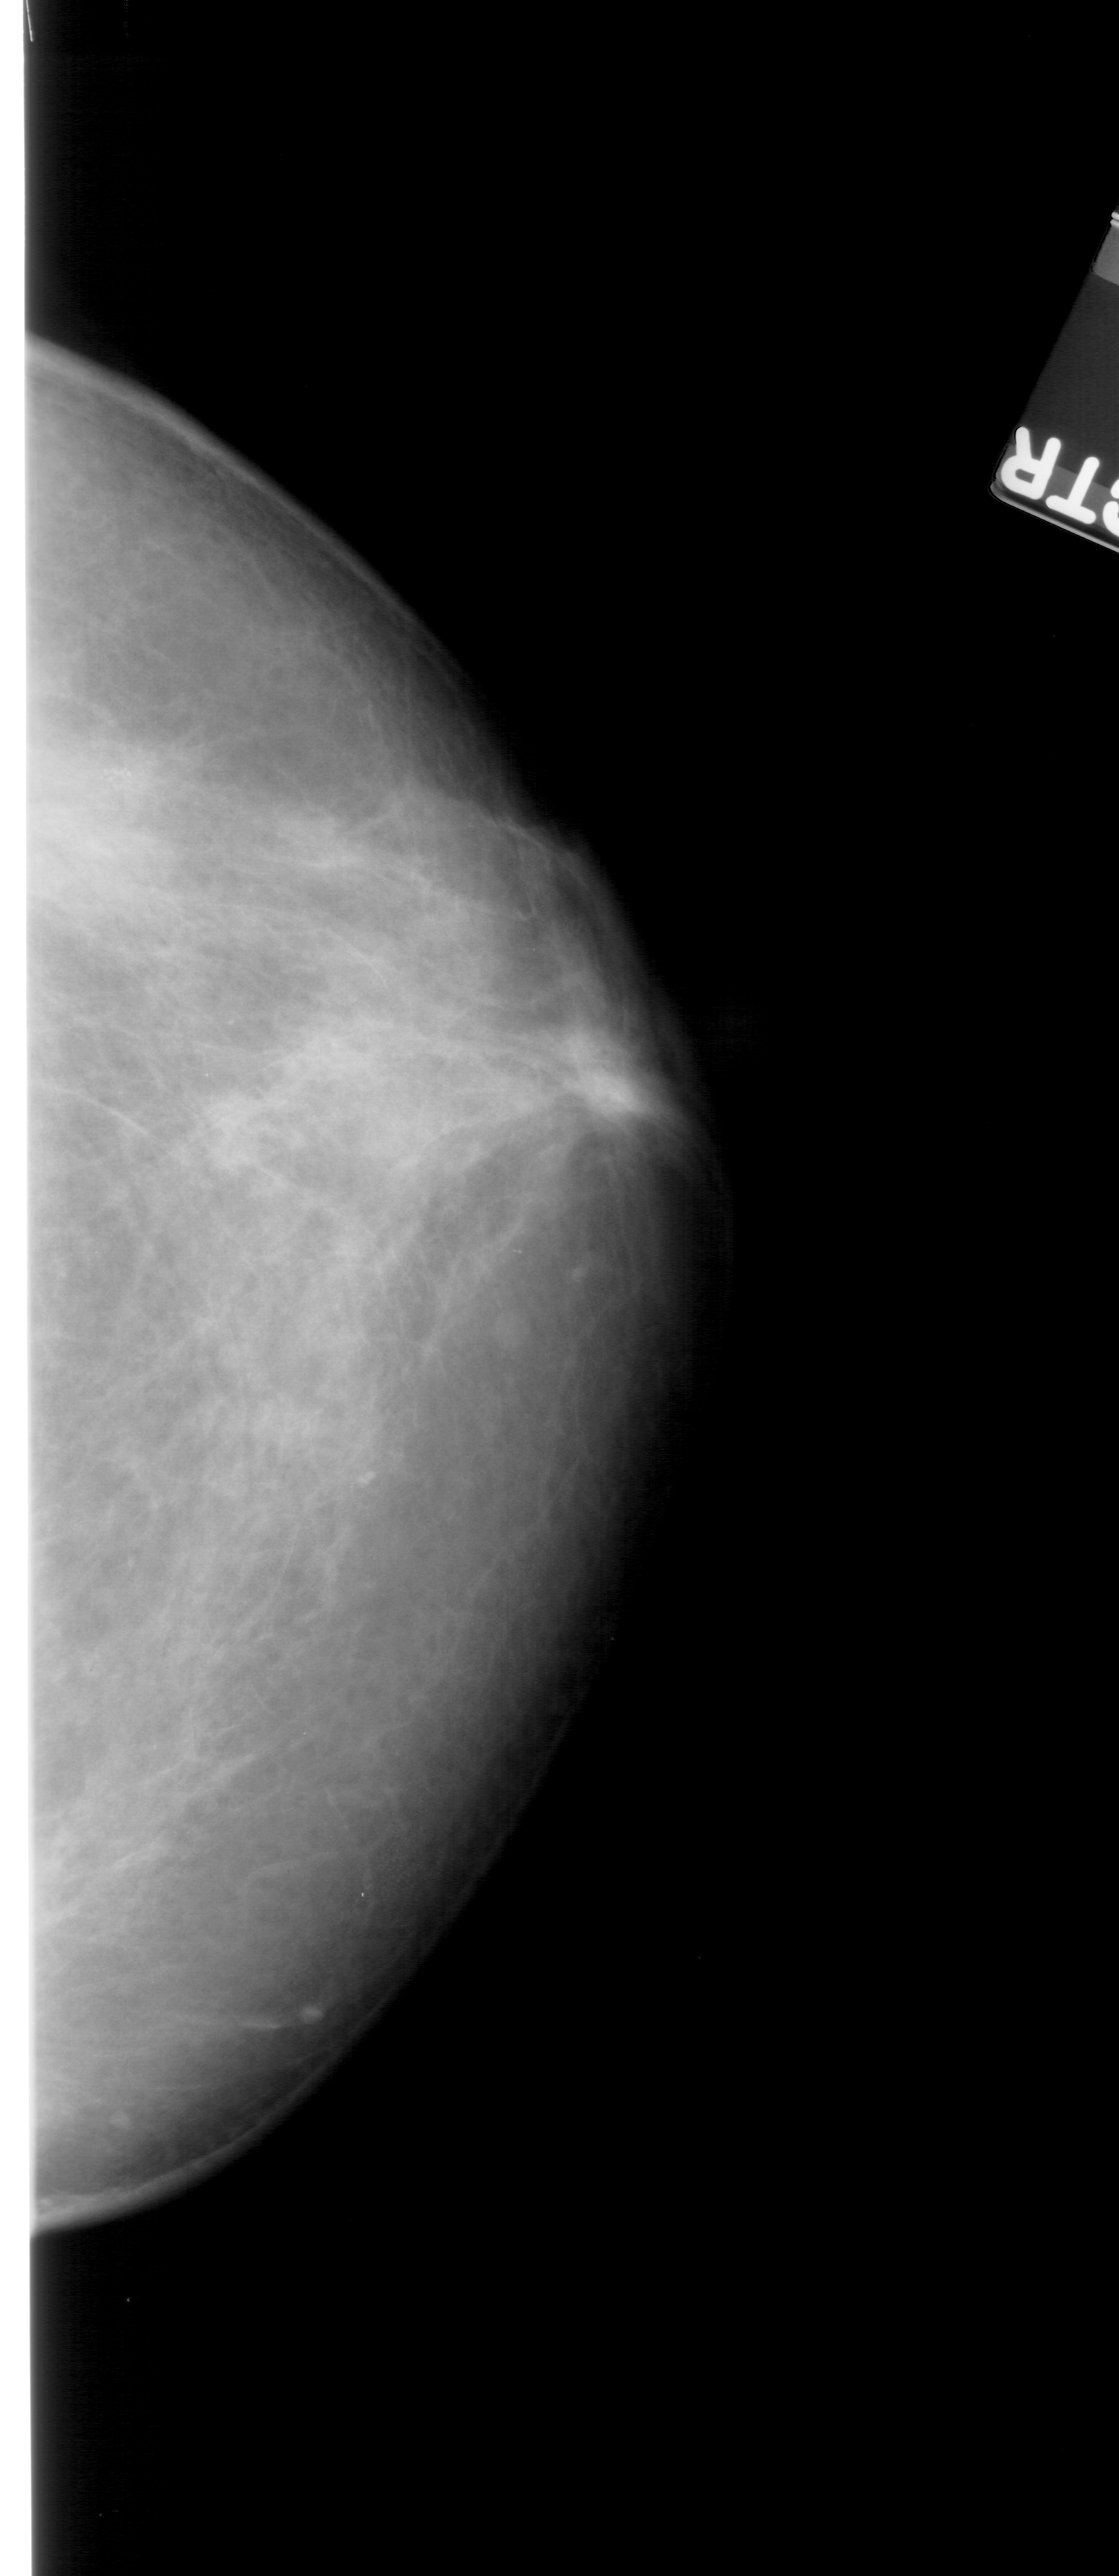
Mammogram (digitized film); right breast; CC view; BI-RADS breast density category 4 (scale 1–4); 1119 × 2576 image matrix.
Expert-marked regions of interest on this image (one box per marked abnormality):
- calcifications, morphology pleomorphic, distribution clustered; BI-RADS assessment category 4; pathology (as recorded): benign: bounding box (x1, y1, x2, y2) in pixels: (50, 729, 233, 867)